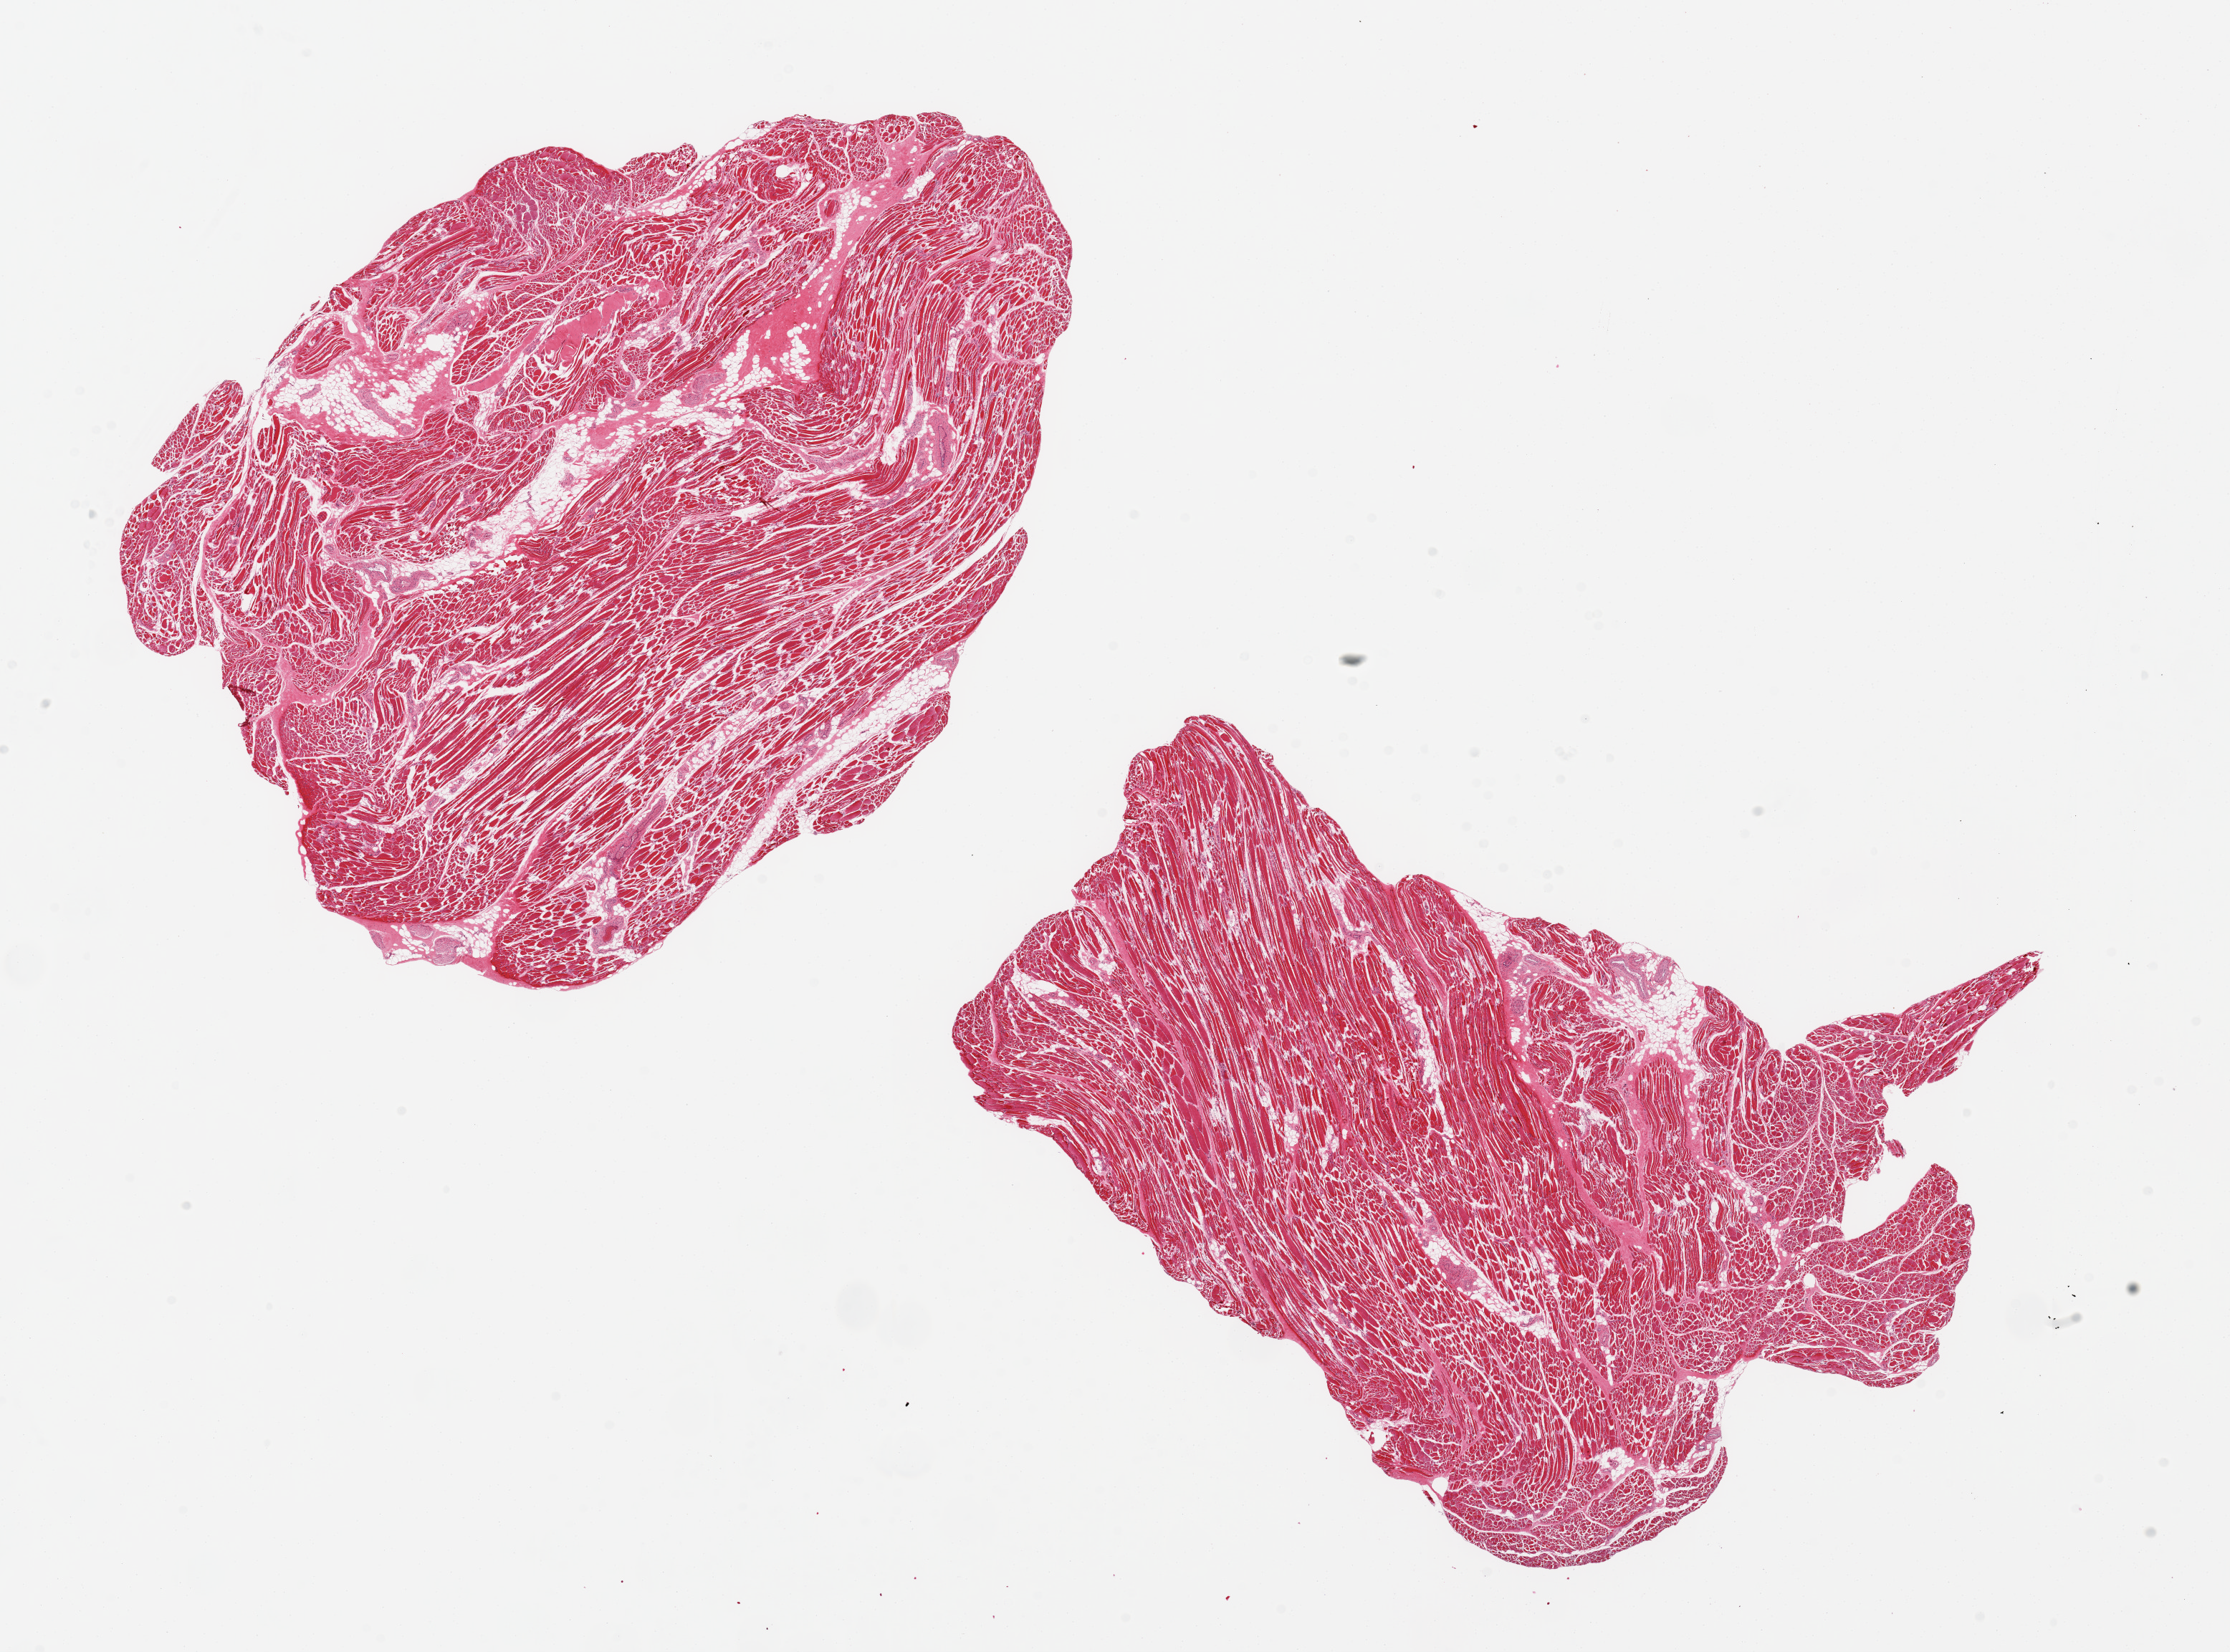
Digitized haematoxylin and eosin-stained section — whole scanned area (about 24.6 x 18.2 mm) shown as a low-resolution overview; PAXgene-fixed paraffin-embedded (PFPE) section; target tissue: skeletal muscle; tissue donor sample. Male donor.
• review note (as recorded): 2 pieces 11x8 & 11x9mm